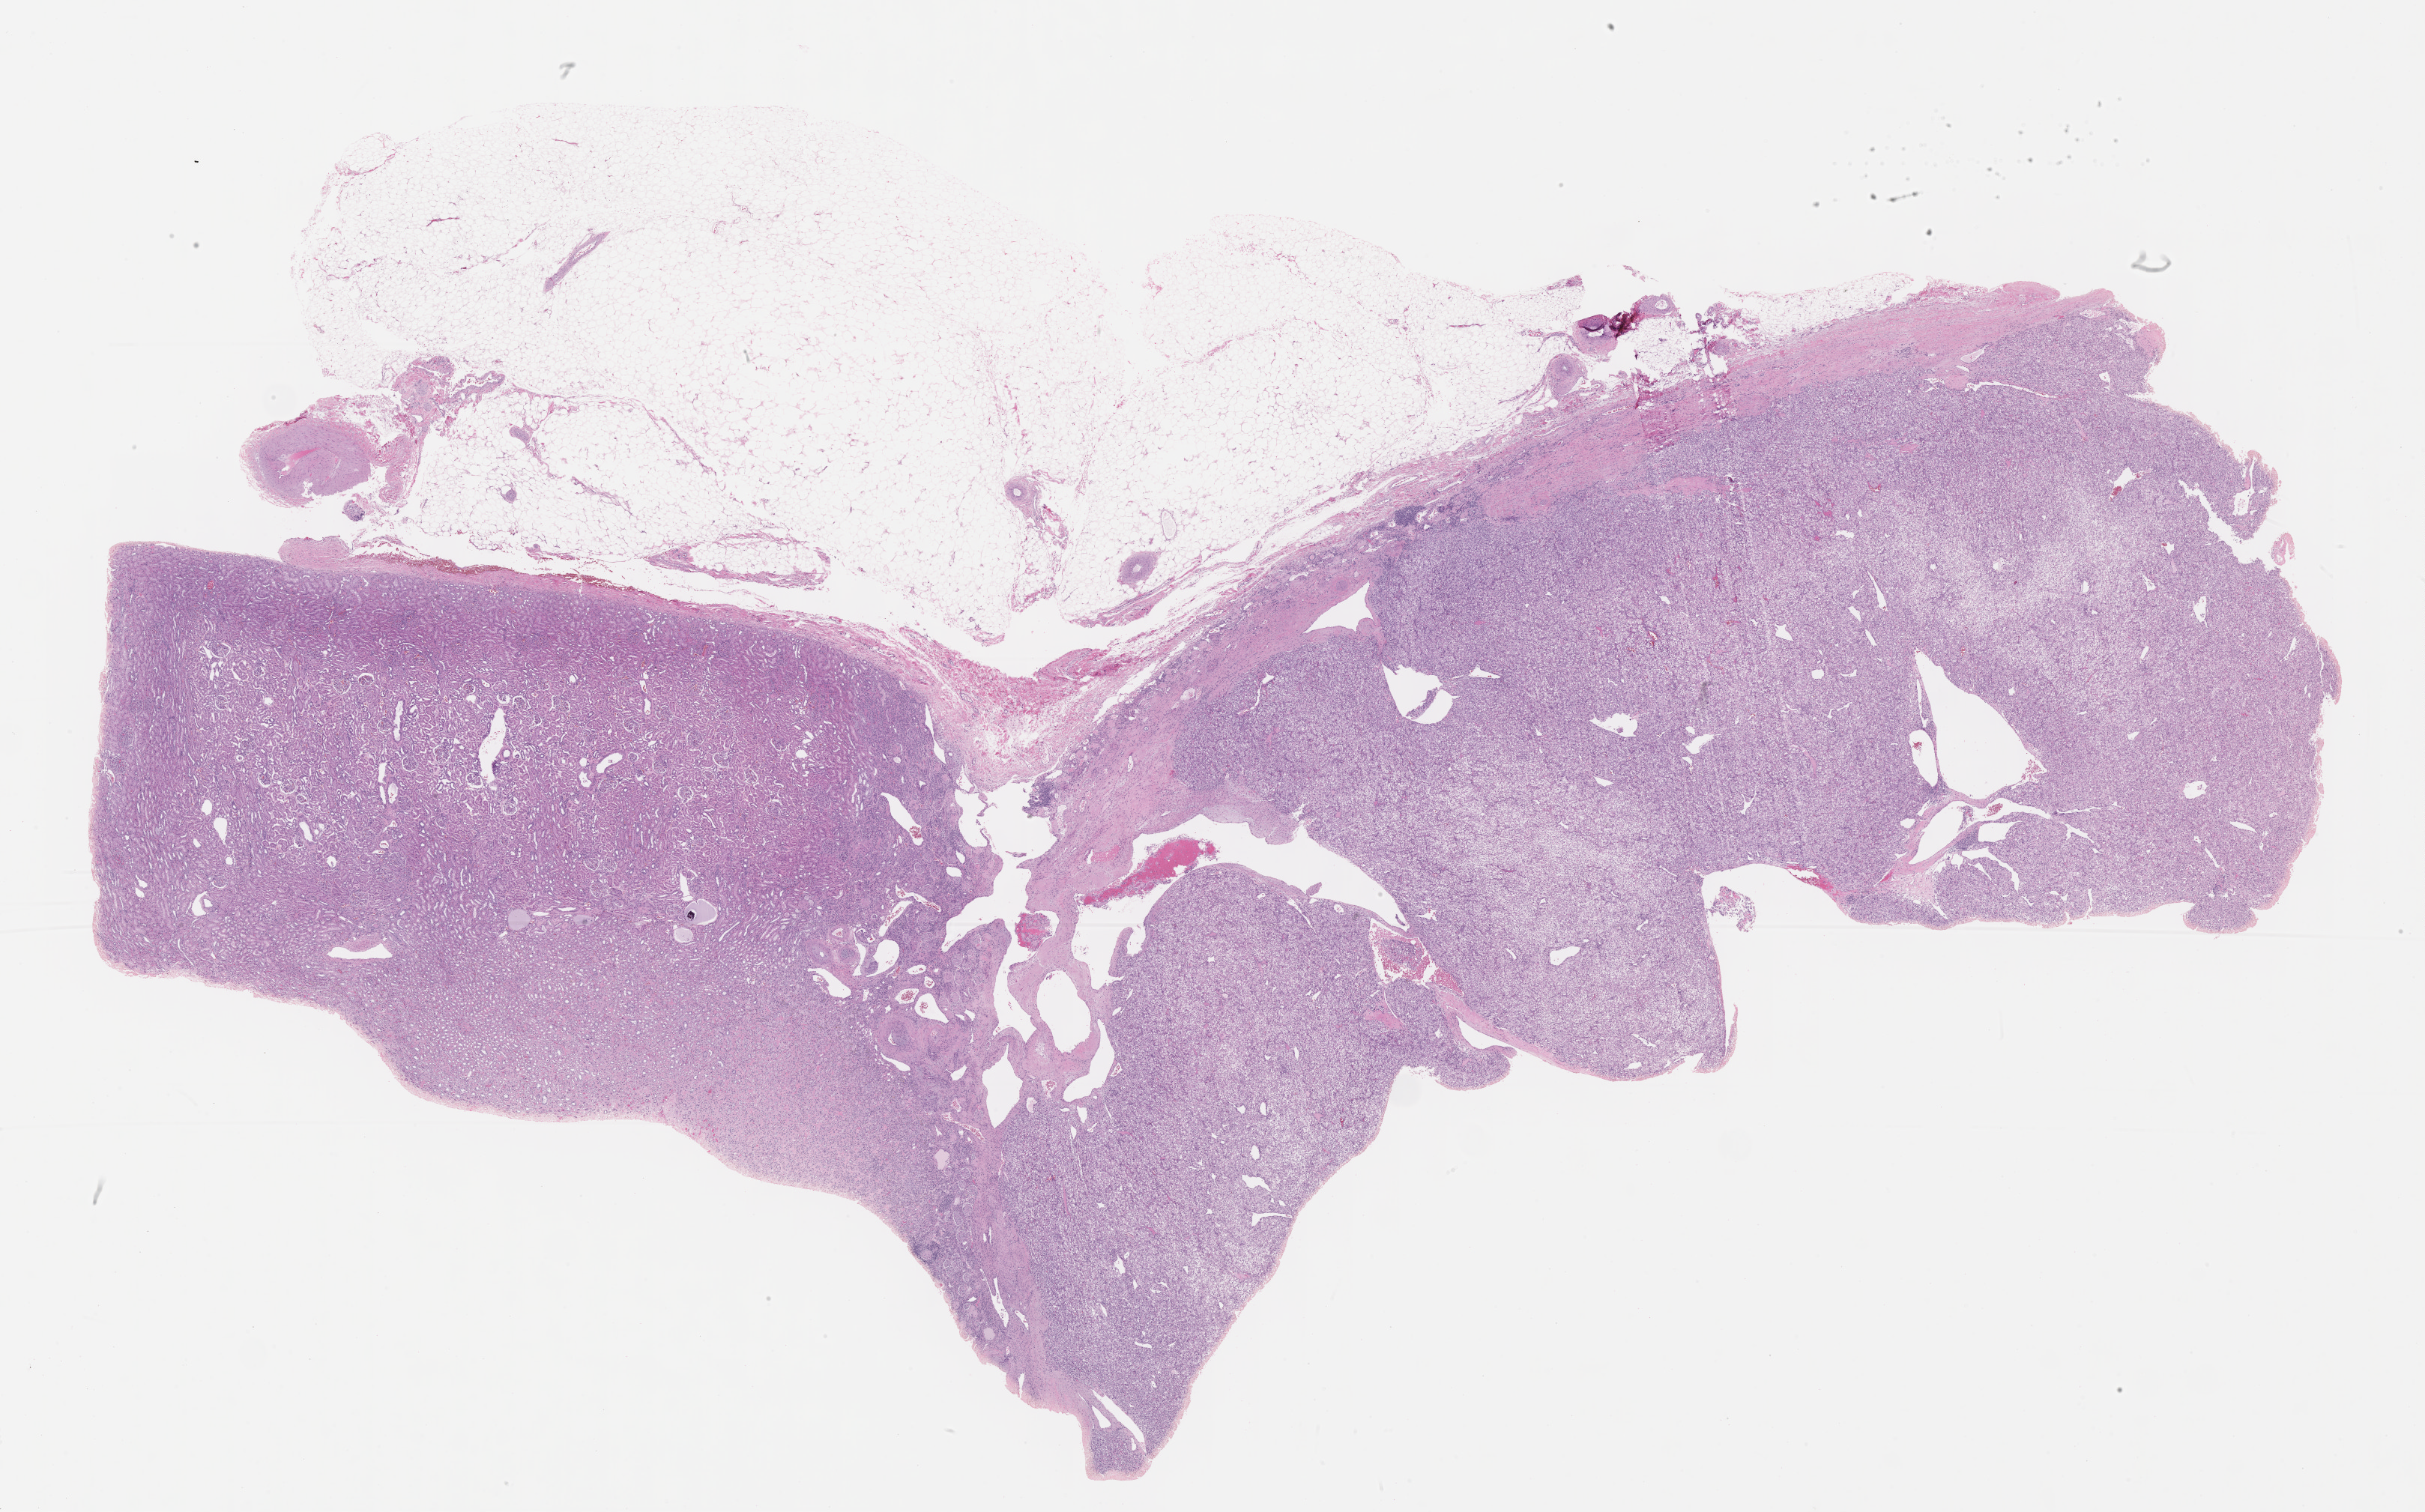
Digitized H&E tissue section (whole slide), whole scanned area (about 26.2 x 16.3 mm, from a 40x scan) shown as a low-resolution overview. Formalin-fixed paraffin-embedded (FFPE) diagnostic section. Kidney, primary tumour sample. Patient: male, age at initial diagnosis 48 years. Histologic grade: G3 (poorly differentiated).
- histologic diagnosis: Clear cell adenocarcinoma, NOS
- AJCC pathologic stage: IV